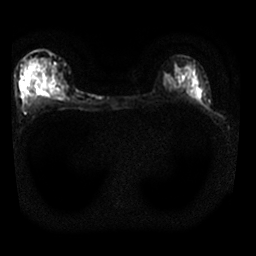
Breast MRI, one axial slice; position 17 of 25 along the scan axis; diffusion-weighted series; image 2 of 4 stored at this slice position (different b-values; order by instance number); 1.5 T; 4 mm slice thickness; 256 × 256 image matrix, field of view 310 × 310 mm. Female patient.
Annotated regions visible in this slice (manually delineated by an expert):
- tumour on diffusion-weighted imaging: bounding box [x1, y1, x2, y2] px = [35, 83, 47, 91]